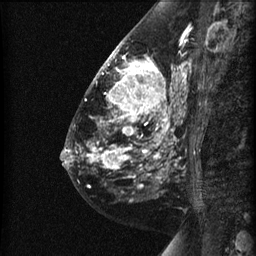
Breast MRI (dynamic contrast-enhanced), one sagittal slice. Slice 25 of 60 in the series (ordered by position). Dynamic contrast-enhanced series, image 2 of 3 at this slice position (ordered by acquisition). 1.5 T. TE 4.2 ms, TR 22.7 ms. 1.5 mm slice thickness. 256 × 256 image matrix. Patient: female, 48 years. Case-level facts recorded for this patient, not image findings: setting: breast cancer imaged before/during neoadjuvant chemotherapy; receptor status: triple-negative.
Structures marked on this image (semi-automatic segmentation, software-assisted and operator-edited):
- analysis volume of interest (the breast-tissue region the enhancement analysis was run in; not a lesion): bounding box [x1, y1, x2, y2] px = [89, 27, 191, 180]
- tumour enhancement mask (voxels above the 90 % enhancement threshold inside the analysis volume of interest): [89, 49, 181, 178]